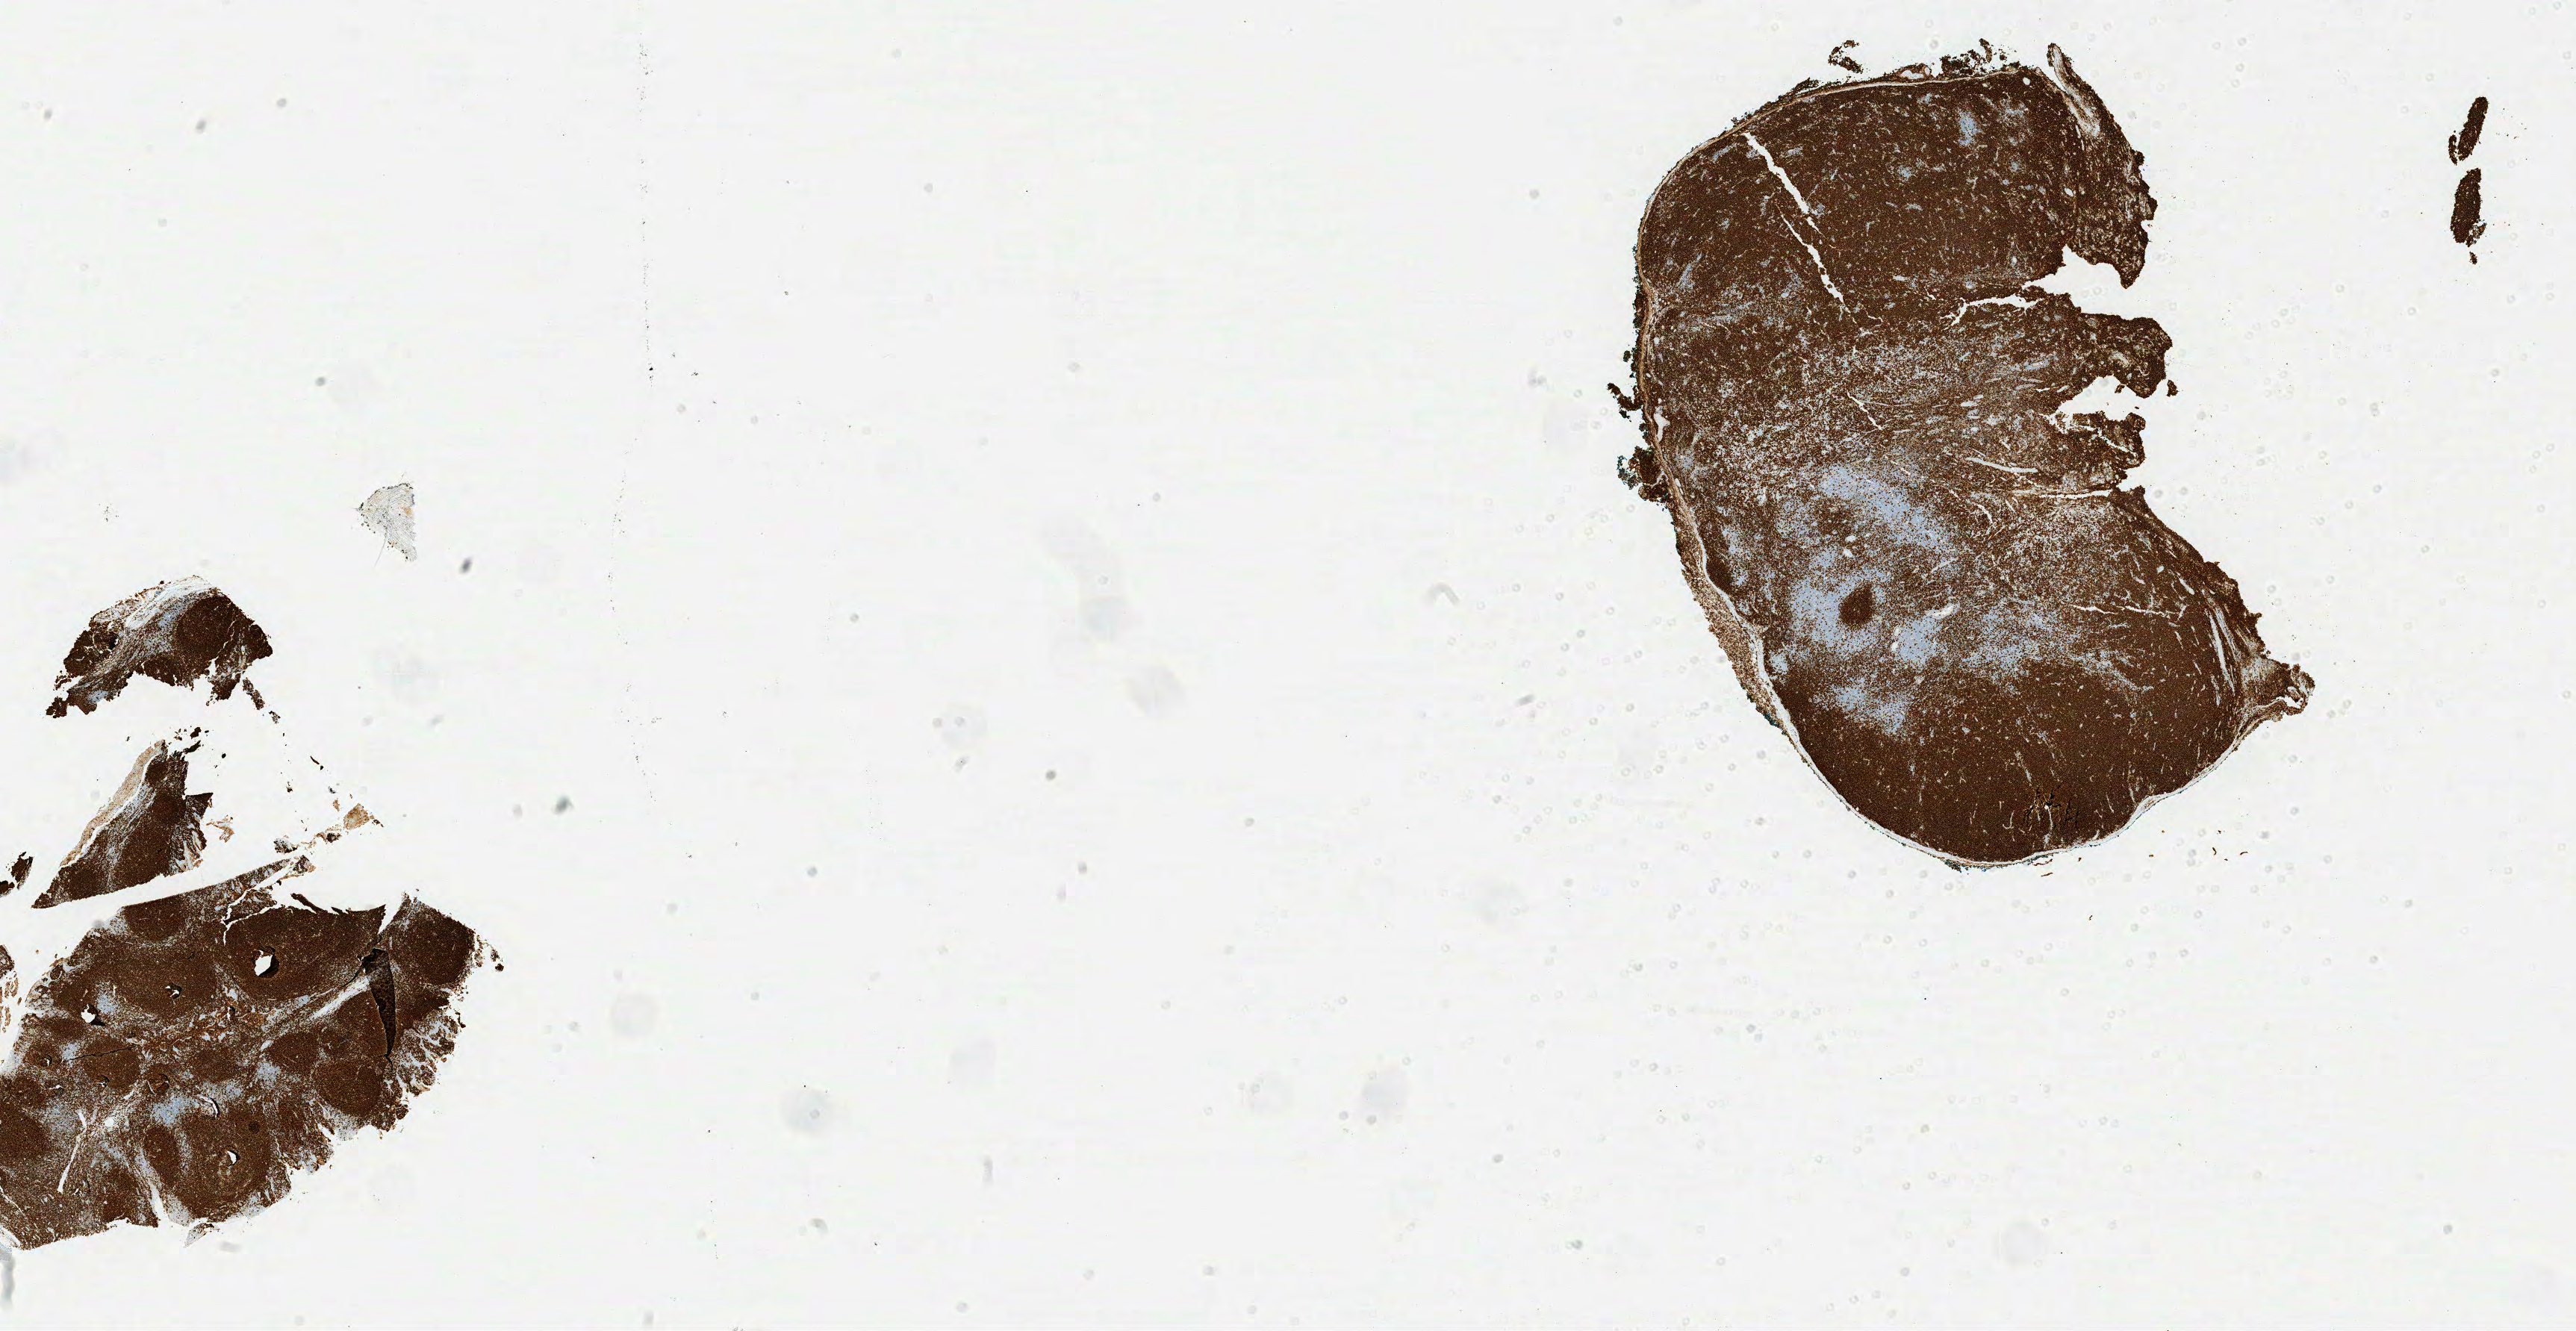
Whole-slide image, immunohistochemical stain for CD20 — low-resolution overview of the scanned area, about 27.5 x 14.2 mm, specimen: tumor tissue. Patient male; age 47 years.
Histologic diagnosis: Burkitt lymphoma, NOS.